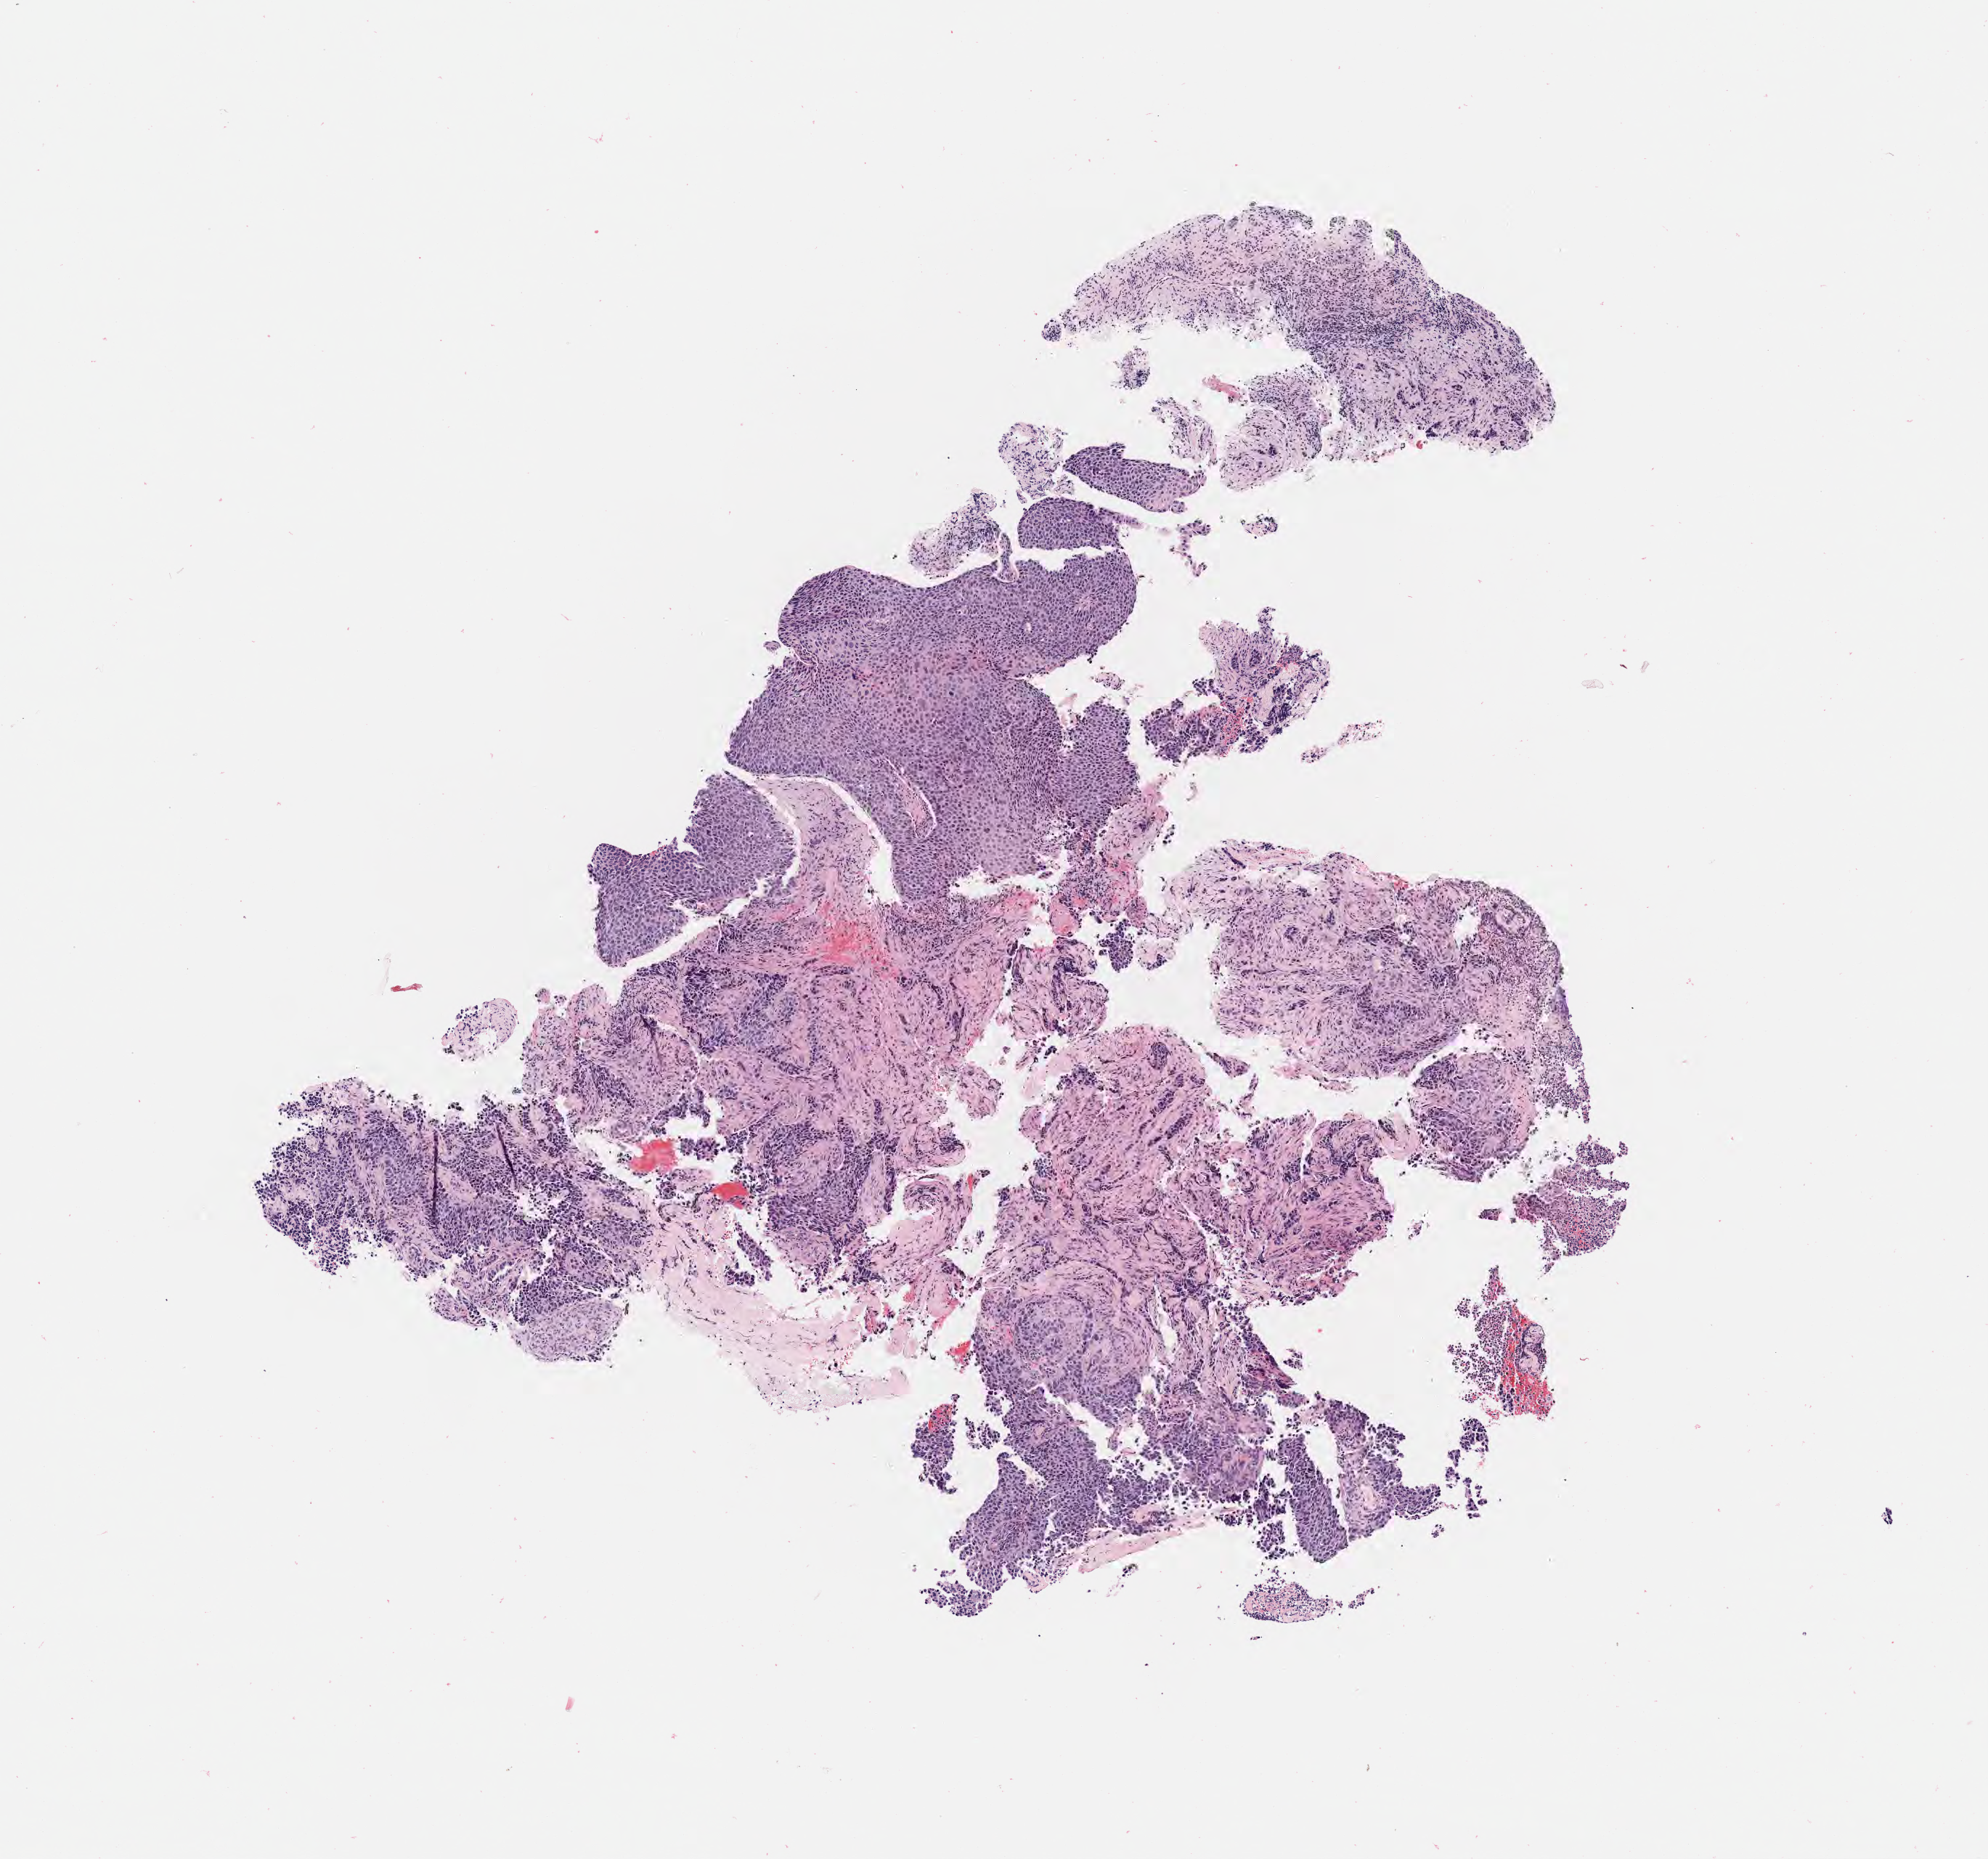
Whole-slide image, haematoxylin and eosin stain, low-resolution overview of the scanned area, about 5.5 x 5.2 mm, tumor tissue, anatomic site: cervix. Patient female; age 30 years.
- histologic diagnosis: Squamous cell carcinoma, large cell, nonkeratinizing, NOS